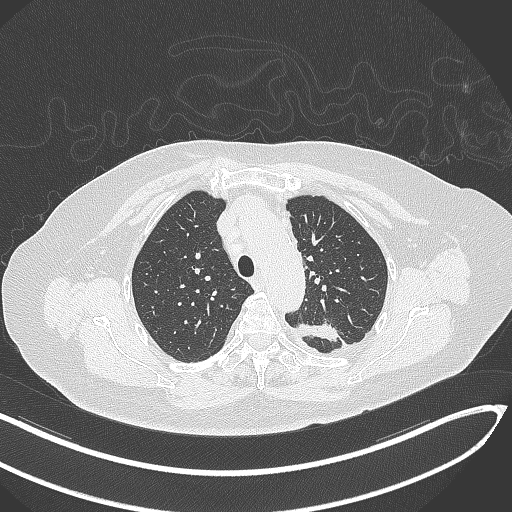
Chest CT, one axial slice; slice 239 of 270 in the series (ordered by position); reconstruction kernel B70f; lung window (W 1500 / L -600 HU); 1 mm slice thickness; 512 × 512 image matrix. Patient: female, 76 years. From the clinical record (not read from this slice): clinical TNM (as recorded): T1c N0 M0.
Structures marked on this image (bounding box drawn by a radiologist):
- lung tumour (recorded histology: adenocarcinoma): bounding box <295,317,339,349> (left, top, right, bottom; pixels)